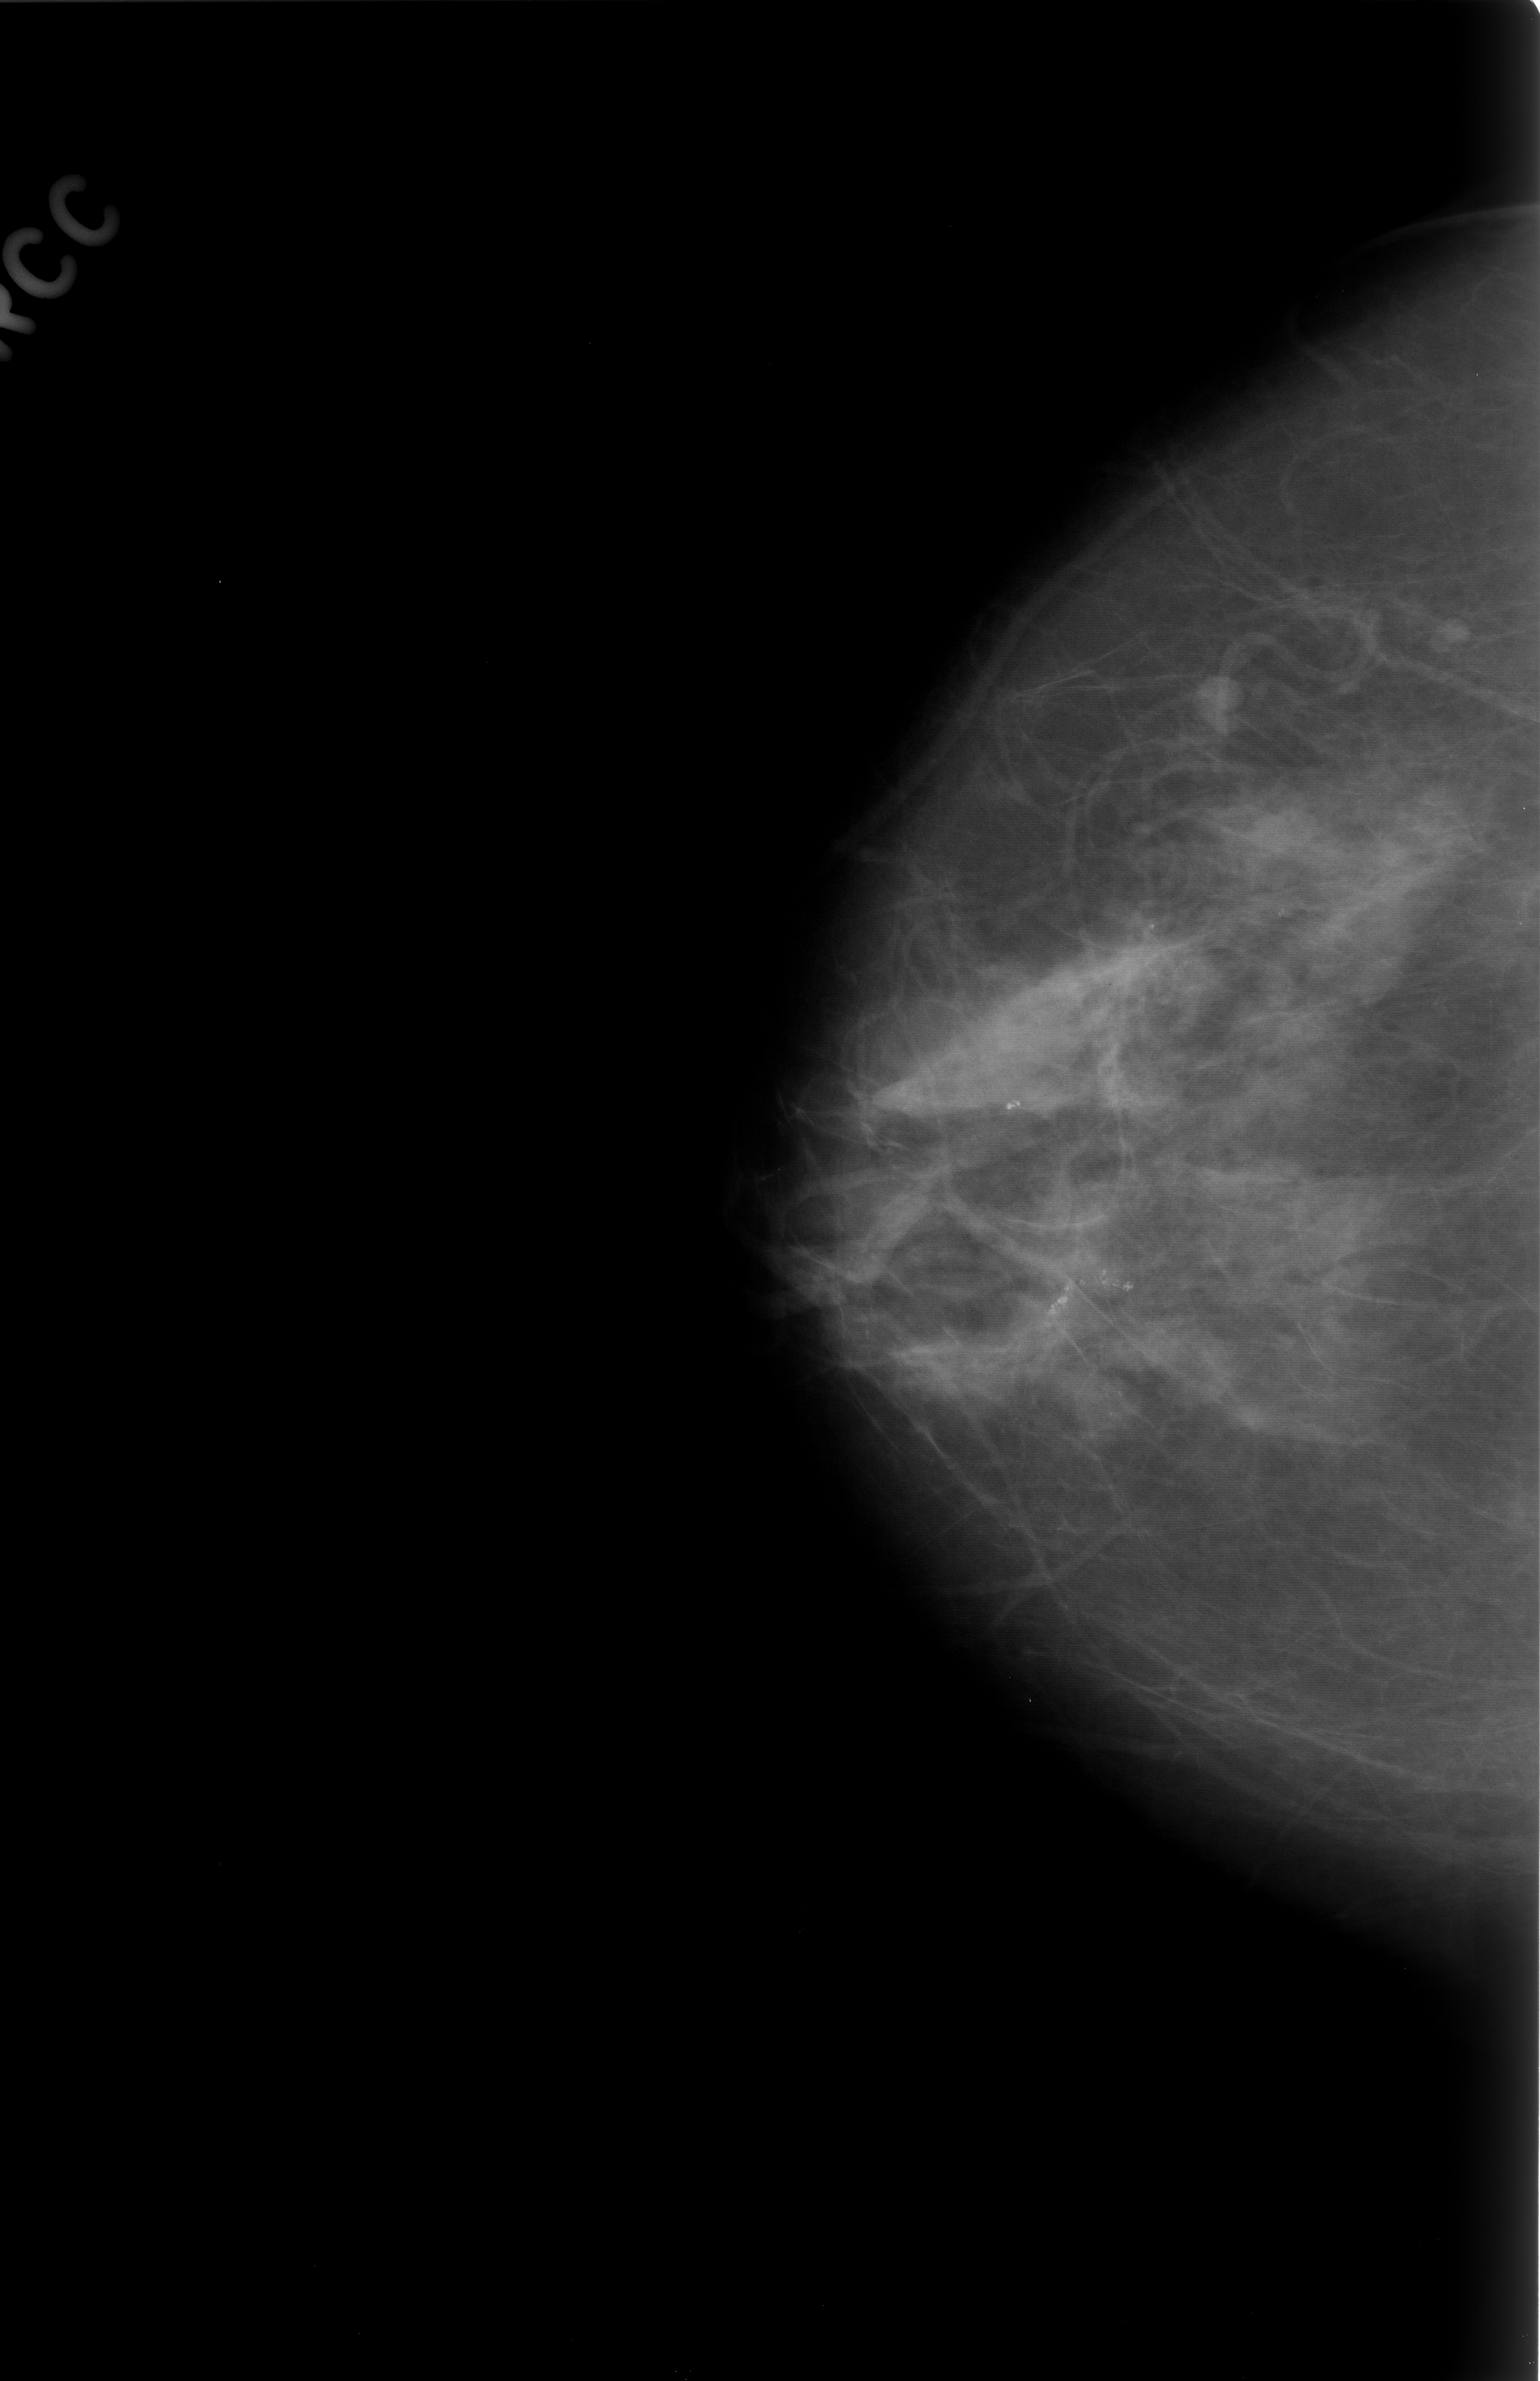
Mammogram (digitized film); right breast; CC view; BI-RADS breast density category 2 (scale 1–4).
Marked findings (only marked abnormalities are described; nothing is implied about the rest of the image): Finding 1 of 2: calcifications, morphology pleomorphic, distribution clustered; BI-RADS assessment category 3; pathology result (as recorded, not read from the image): benign. Finding 2 of 2: calcifications, morphology pleomorphic, distribution clustered; BI-RADS assessment category 4; subtlety rating 5 on a 1 (subtle) to 5 (obvious) scale; pathology result (as recorded, not read from the image): benign.